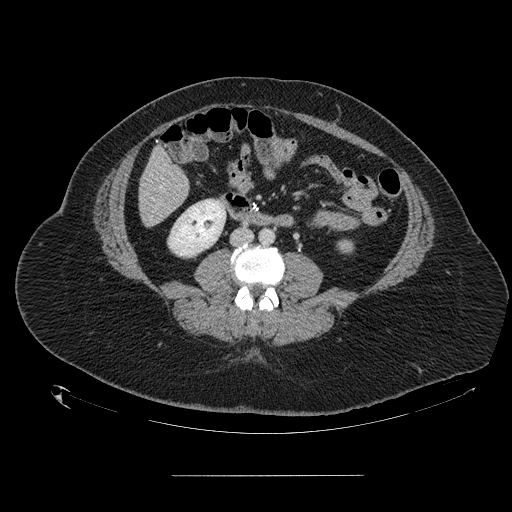
Contrast-enhanced abdominal CT, one axial slice; position 29 of 164 along the scan axis; intravenous contrast given; soft-tissue window (W 400 / L 40 HU); 2.5 mm slice thickness; 512 × 512 image matrix, field of view 495 × 495 mm. Female patient, age 52 years. Case-level facts recorded for this patient, not image findings: diagnosis: colorectal cancer liver metastases, imaged before liver resection; multiple liver metastases: yes; largest metastasis: 3.5 cm.
Structures marked on this image (manually delineated by an expert):
- hepatic veins: bounding box [x1, y1, x2, y2] px = [160, 187, 162, 189]
- liver: [141, 150, 189, 226]